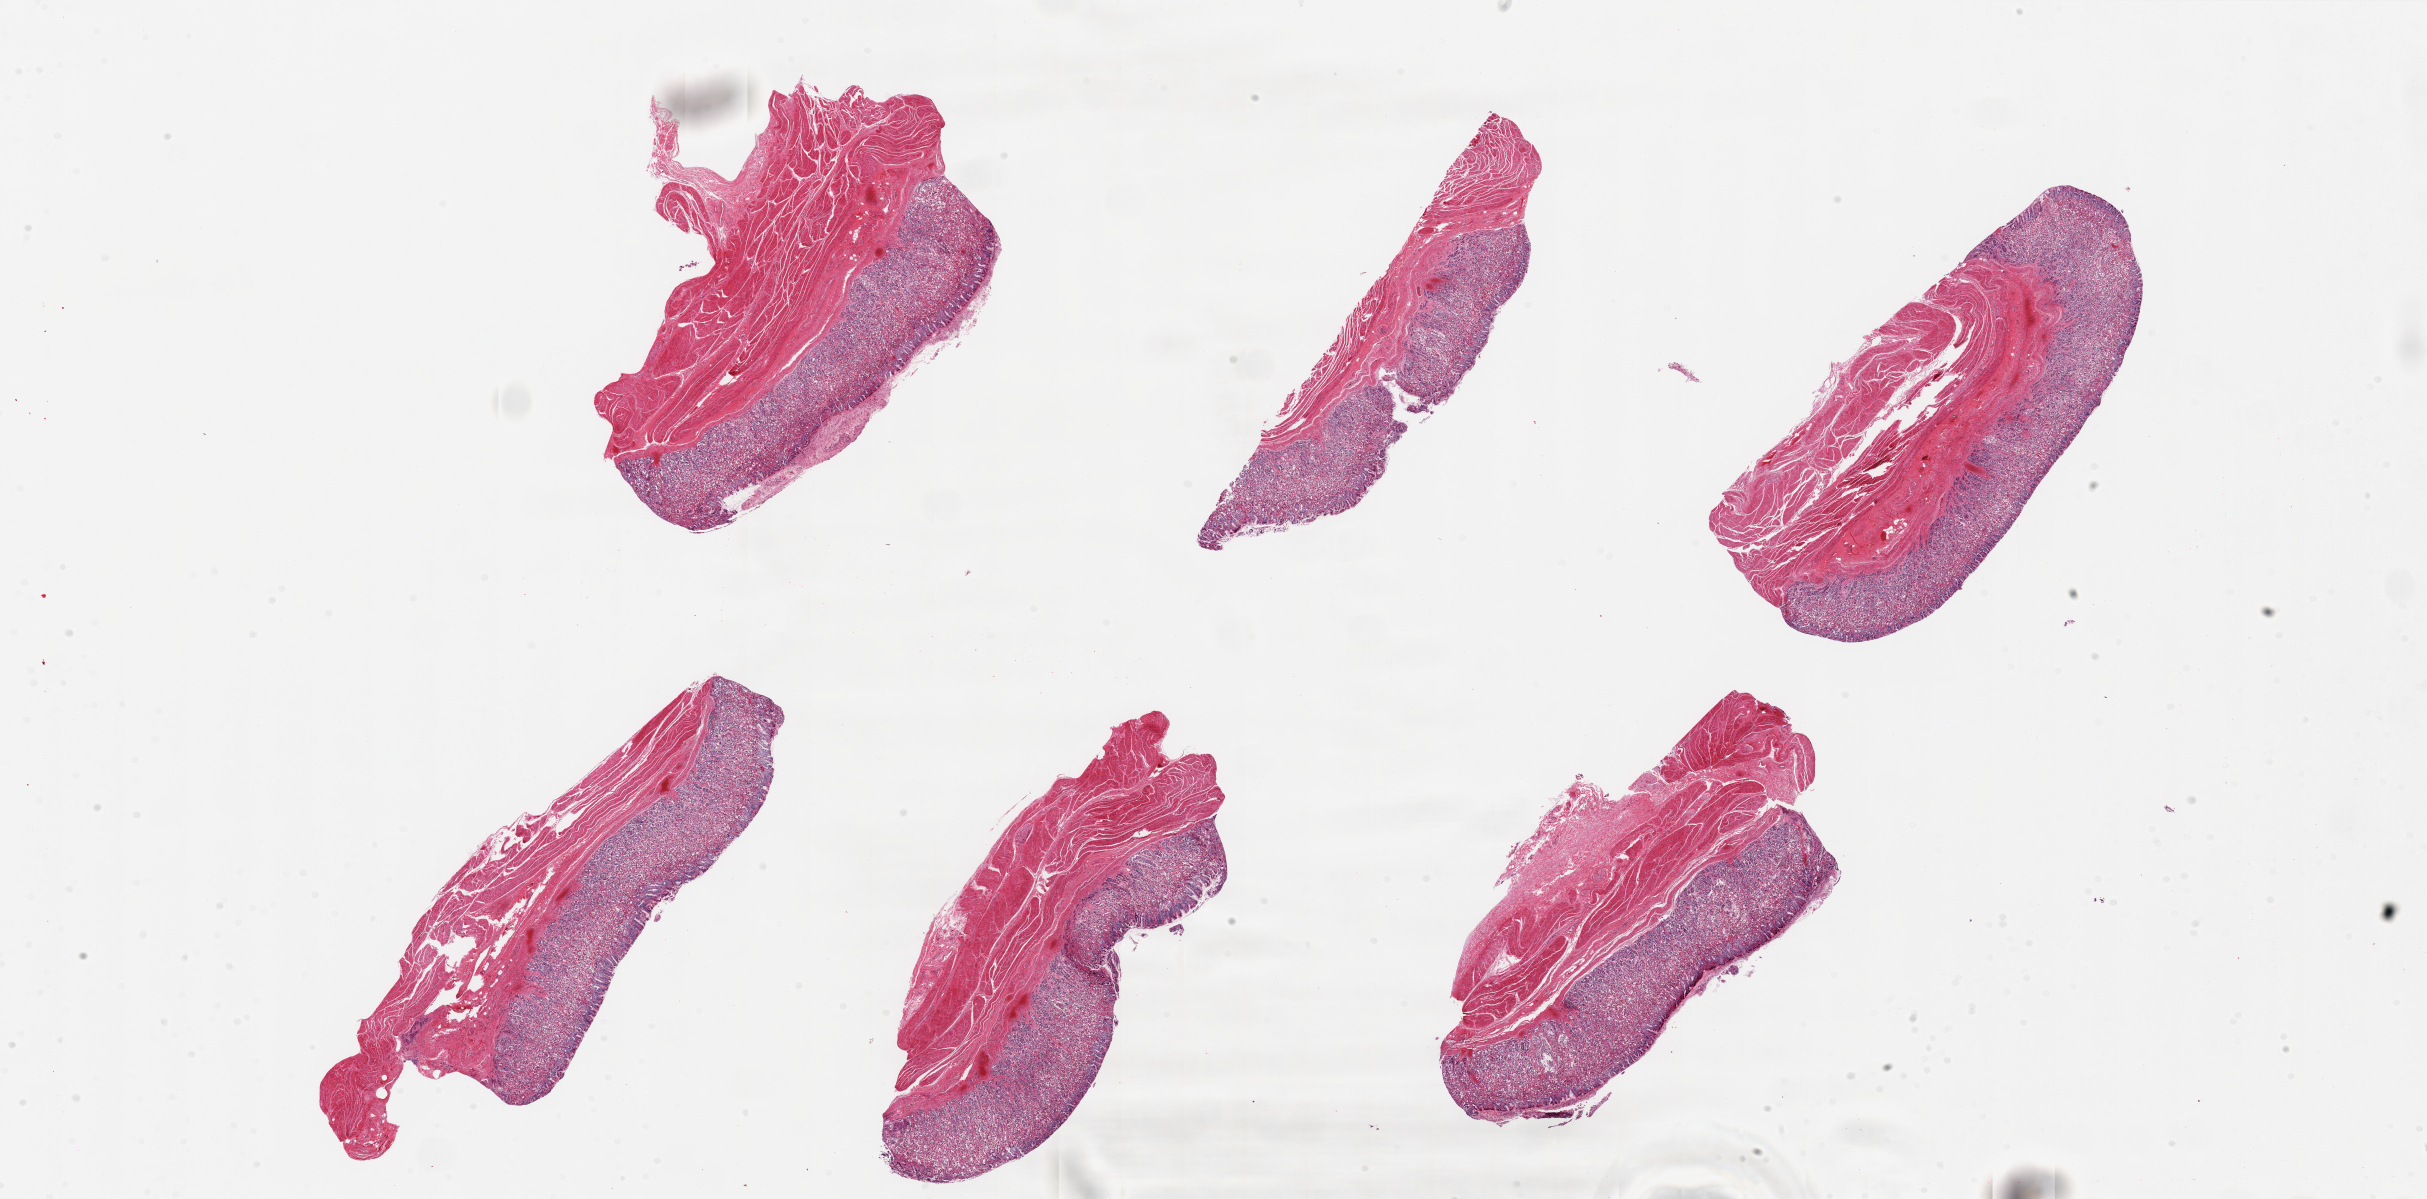
H&E whole-slide image, a low-resolution overview of the entire scanned area, about 38.4 x 19.0 mm; PAXgene-fixed, paraffin-embedded tissue; sampled site (target tissue): stomach; donor tissue sample. Female donor.
• pathologist's review note for this sample: 6 pieces ~8x3mm. Mucosa moderatly autolyzed but intact, up to 40-50% thickness